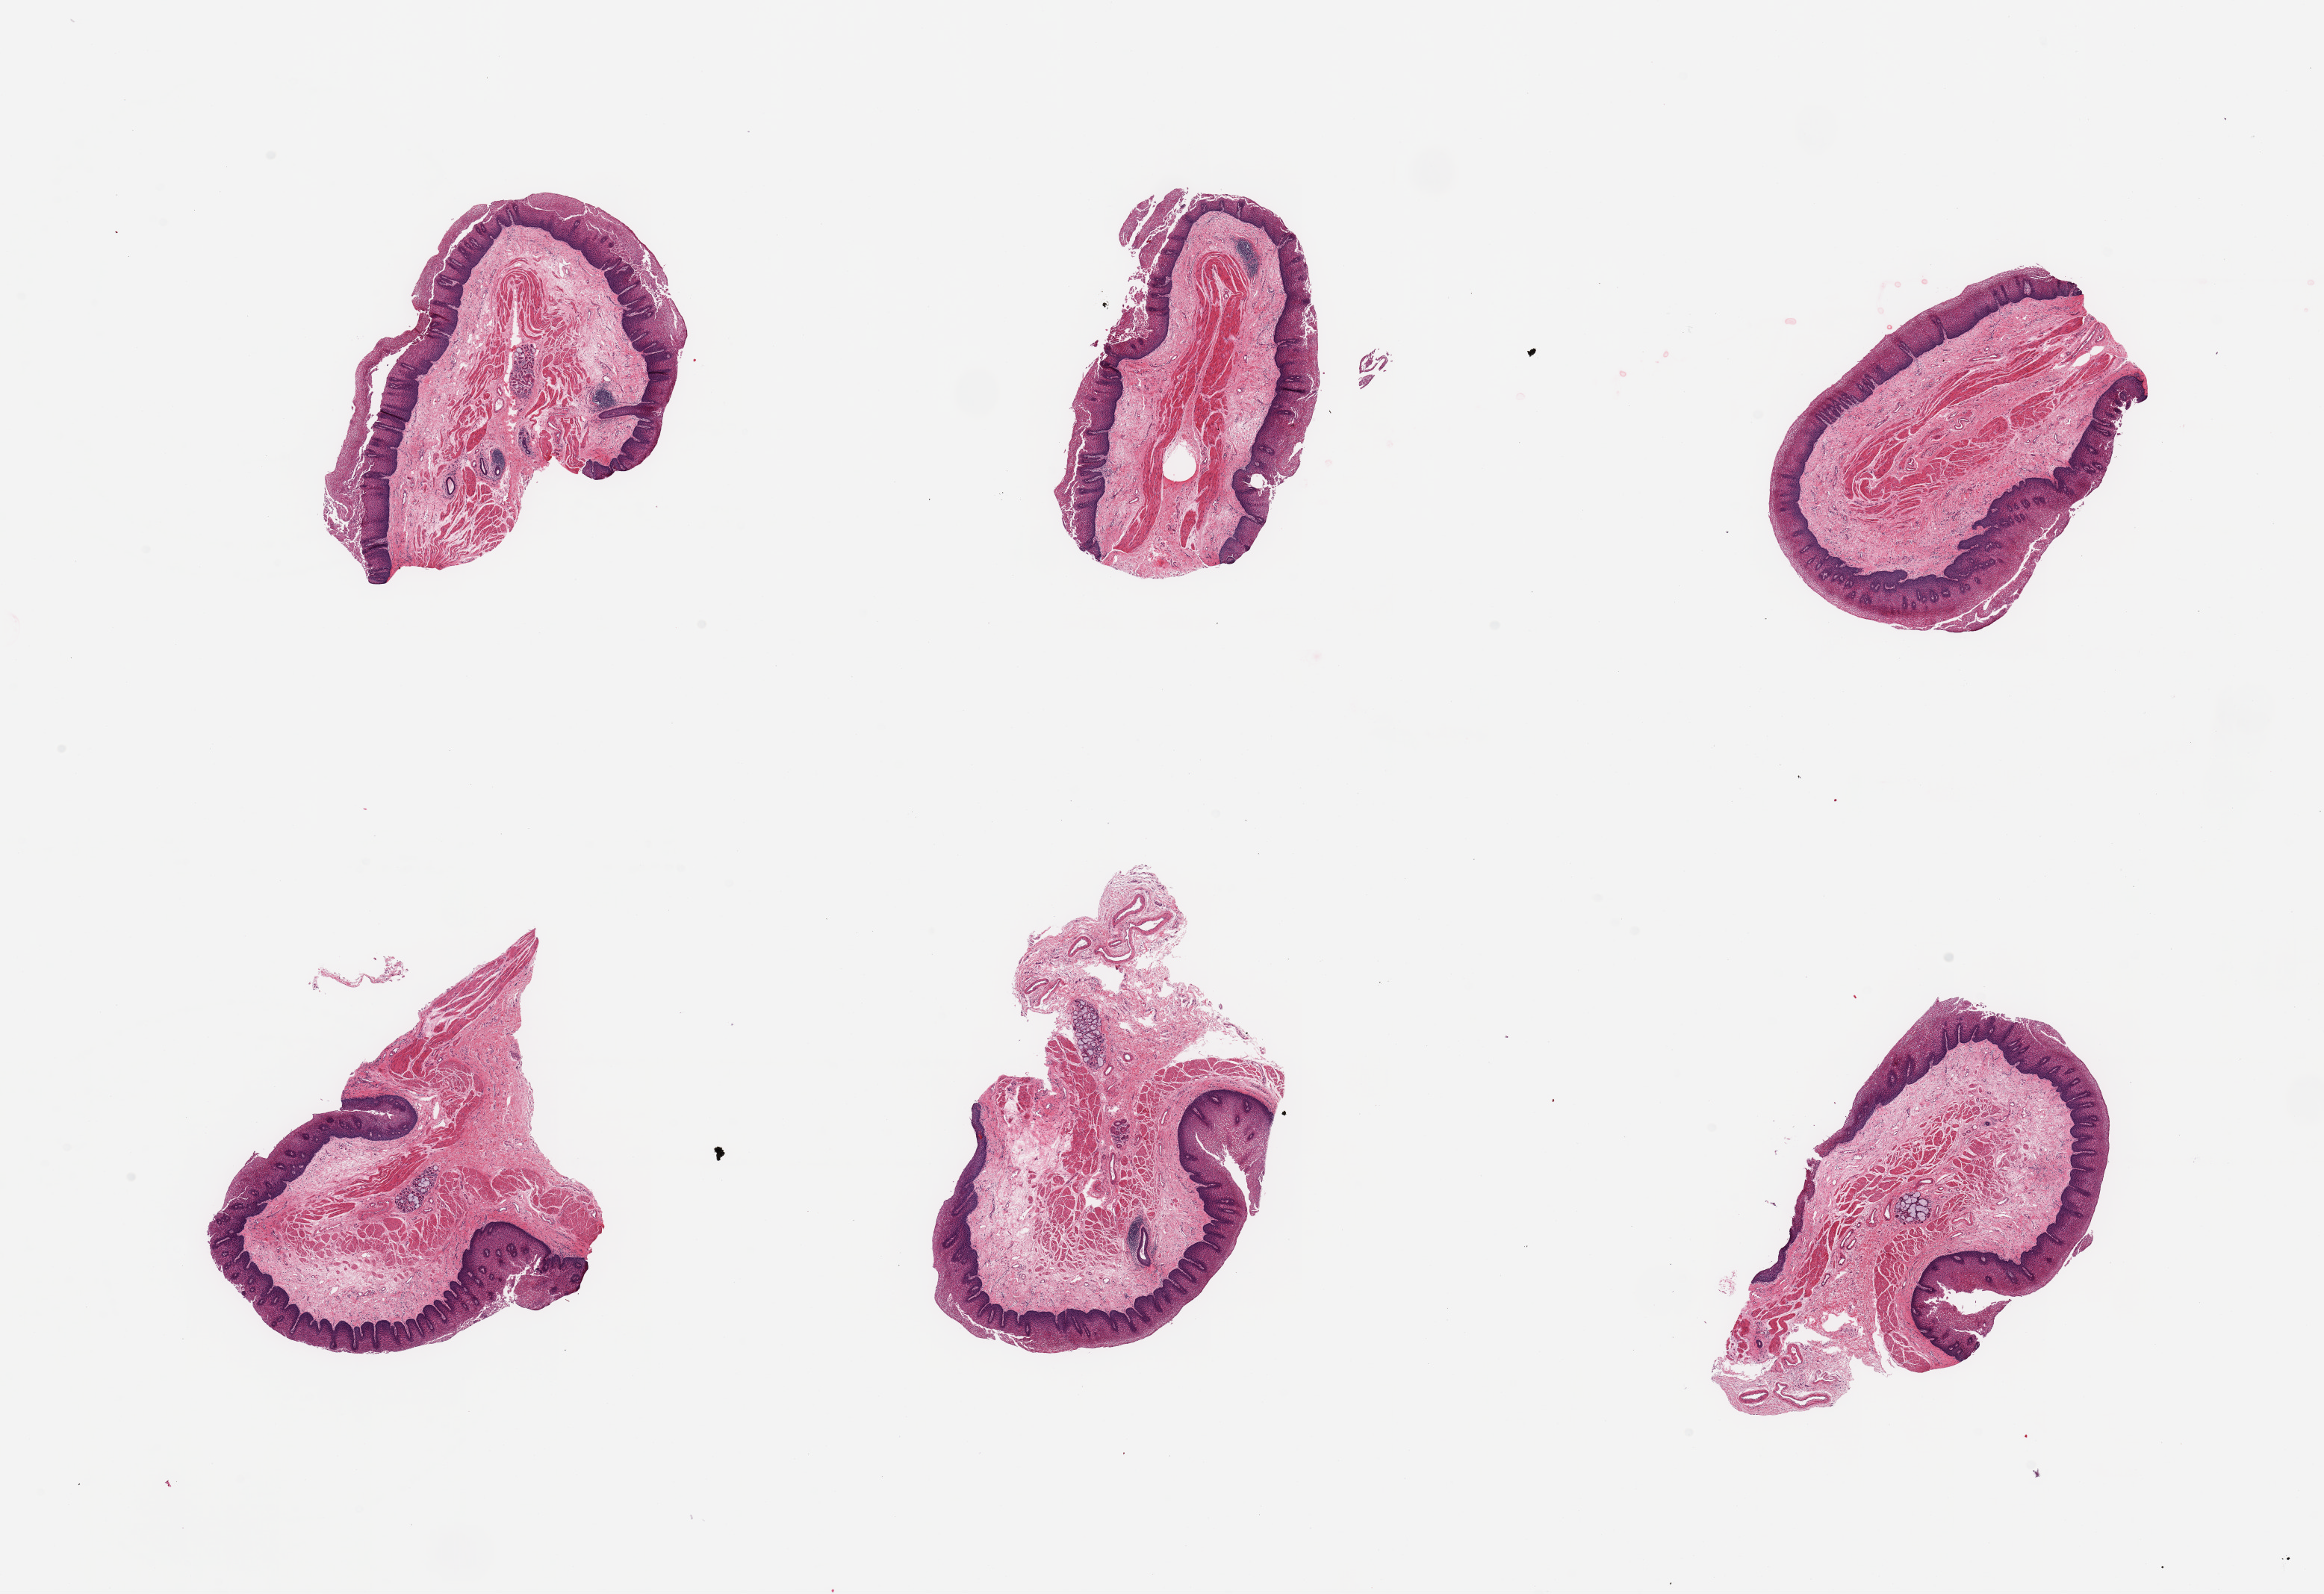
H&E whole-slide image — a low-resolution overview of the entire scanned area, about 24.6 x 16.9 mm (slide scanned at 20x), PAXgene-fixed paraffin-embedded (PFPE) section, target tissue: esophageal mucous membrane, tissue donor sample. Donor sex: male.
* reviewer comment on this tissue sample: 6 pieces; squamous hyperplasia consistent with reflux; superficial sloughing